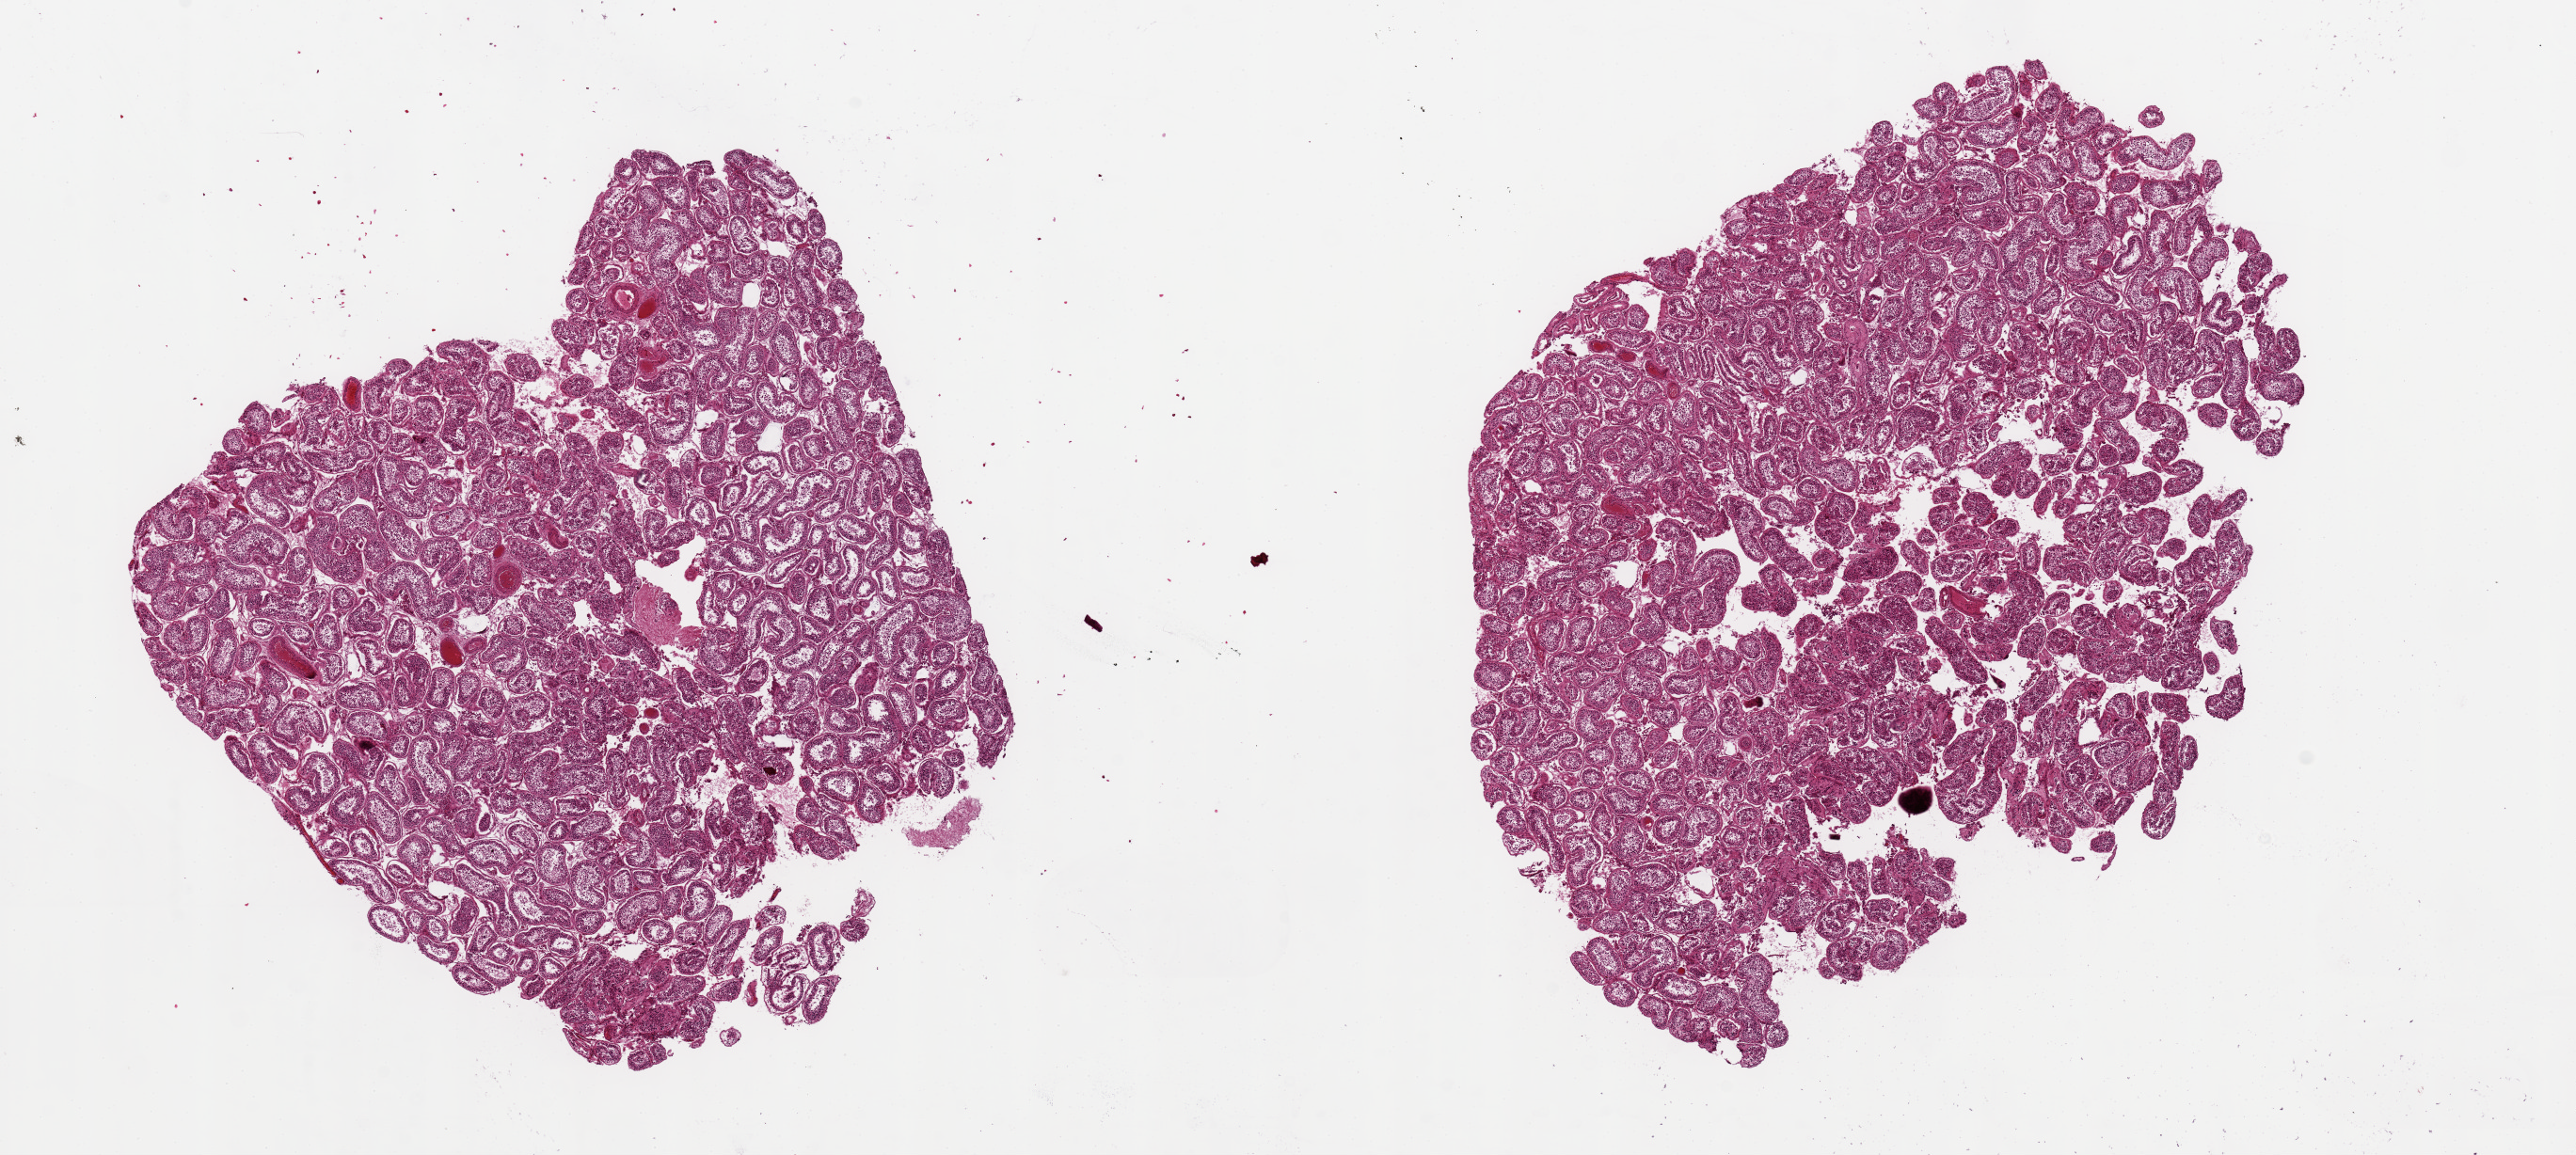
Digitized hematoxylin and eosin (H&E)-stained section — low-resolution overview of the scanned area, about 21.7 x 9.7 mm; PAXgene-fixed, paraffin-embedded tissue; sampled site (target tissue): testis; tissue donor sample.
Review note (as recorded): 2 aliquots, ~6x5mm.